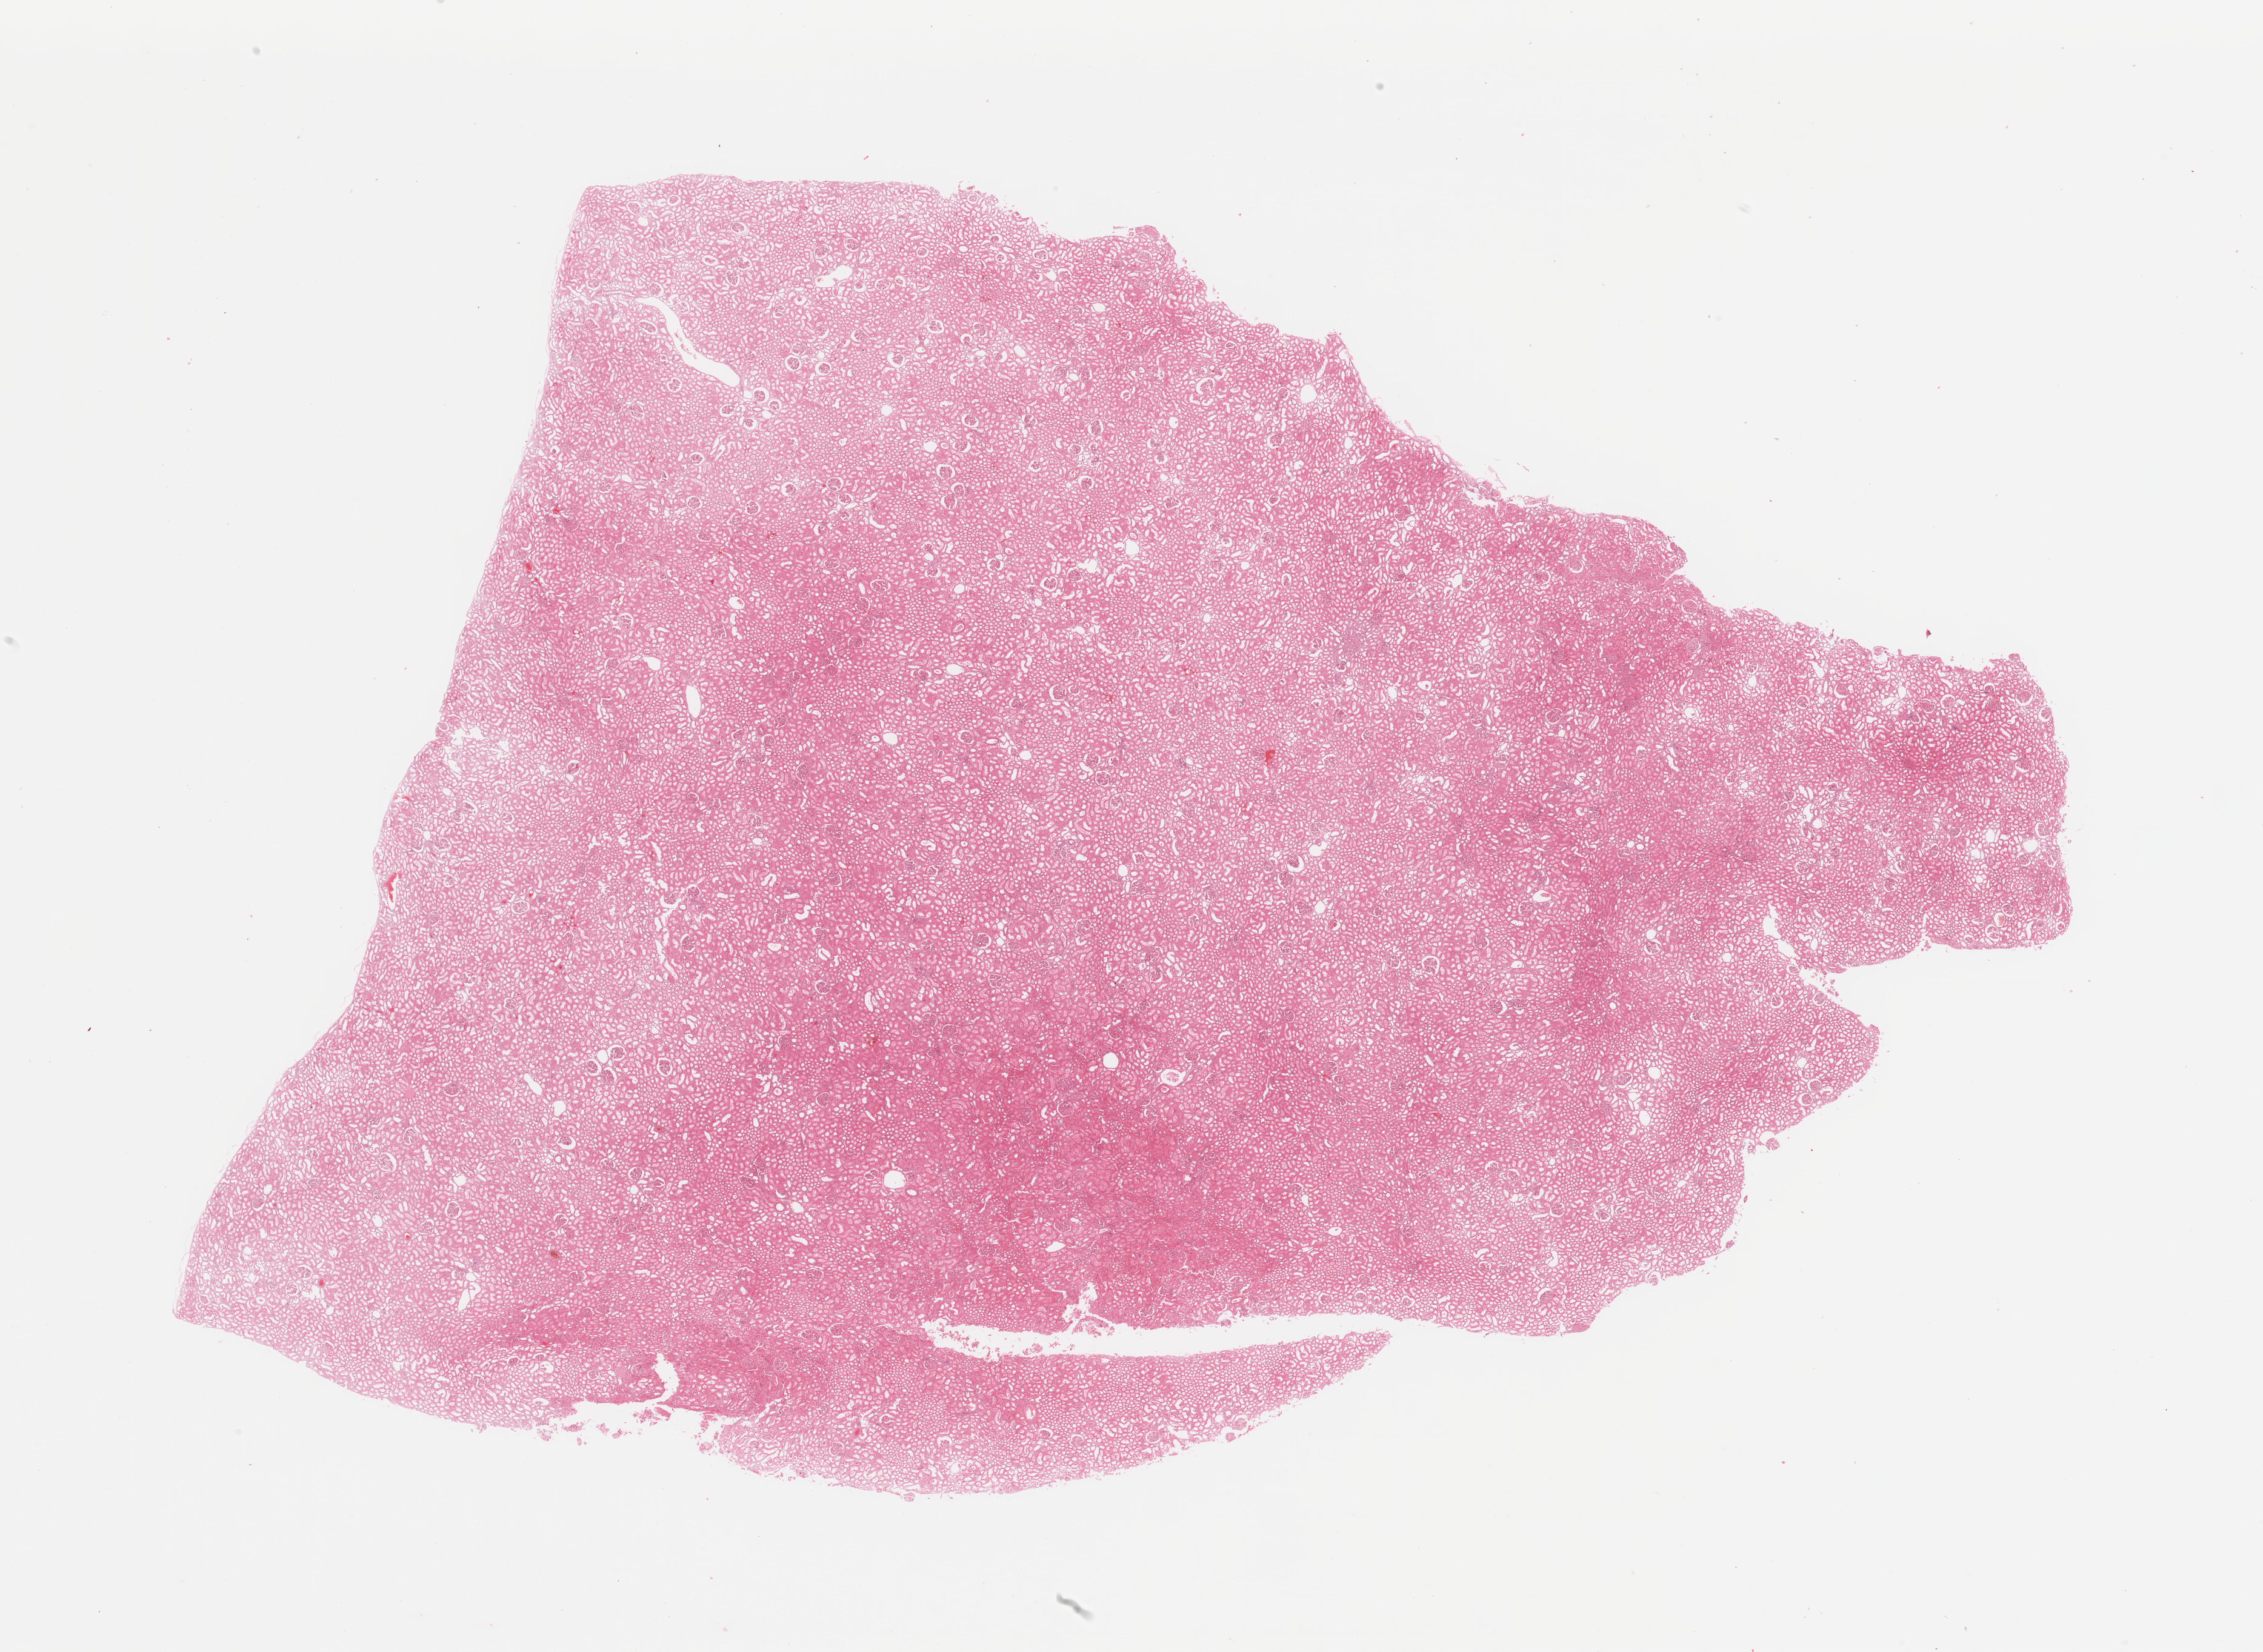
Digitized Hematoxylin and eosin (H&E) stained tissue section (whole slide), whole scanned area (about 29.5 x 21.6 mm) shown as a low-resolution overview; kidney, normal (non-tumour) tissue. Patient: female, age 41 years.
This section: normal (non-tumour) tissue from the same patient. Patient diagnosis: Renal cell carcinoma, NOS.